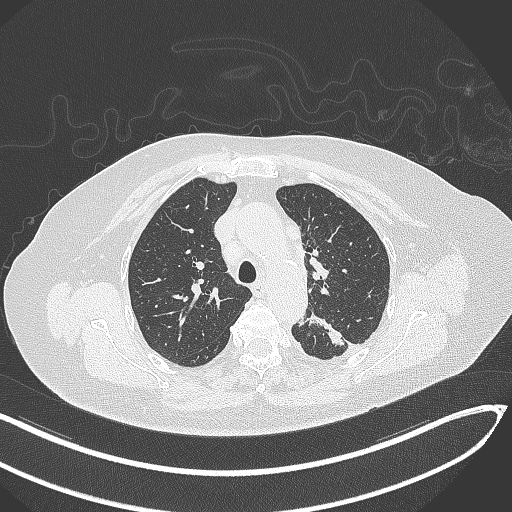
Chest CT, one axial slice. Position 225 of 270 along the scan axis. Lung window (W 1500 / L -600 HU). 1 mm slice thickness. 512 × 512 image matrix. Patient: female, 76 years. Case-level facts recorded for this patient, not image findings: clinical TNM (as recorded): T1c N0 M0.
Outlined on this slice (bounding box drawn by a radiologist):
- lung tumour (recorded histology: adenocarcinoma): bounding box (x1, y1, x2, y2) in pixels: (304, 314, 351, 352)